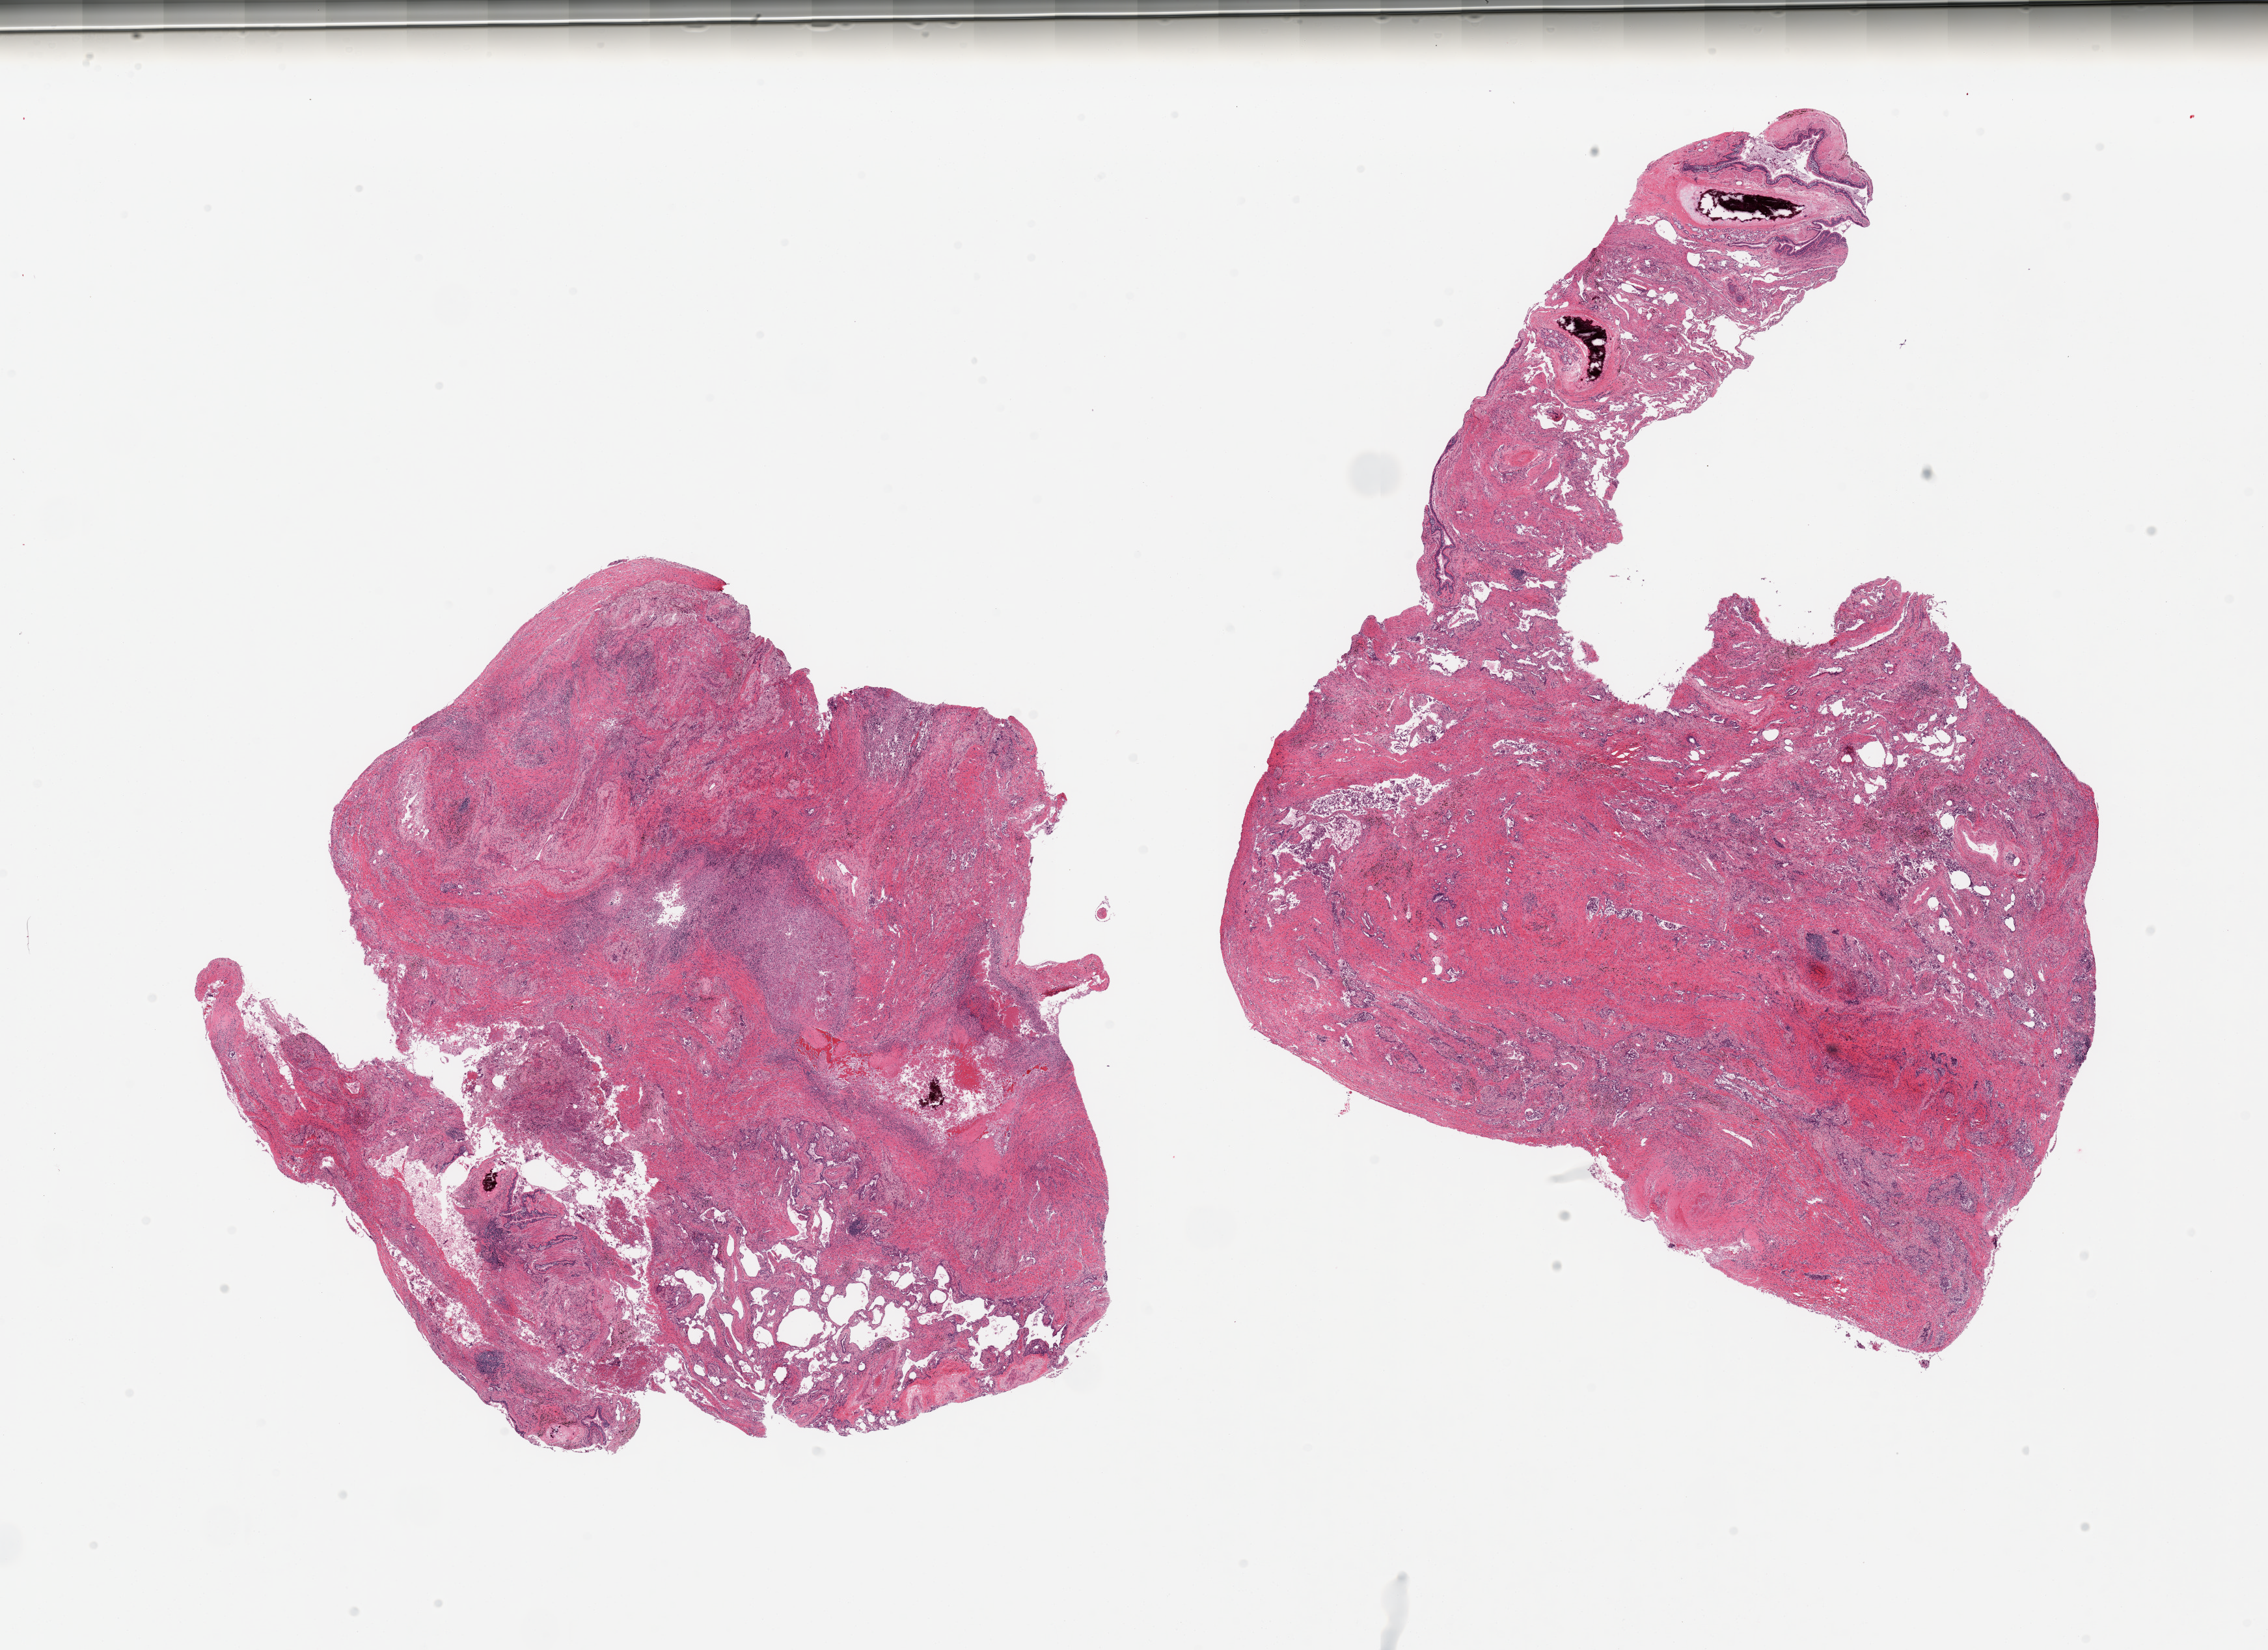
Whole-slide image, H&E stain, brightfield, low-resolution overview of the scanned area, about 27.6 x 20.1 mm (acquisition: 20x scan); PAXgene-fixed paraffin-embedded (PFPE) section; sampled site (target tissue): lung; tissue donor sample.
Pathologist's review note for this sample: 2 pieces diffuse fibrosing and acute pneumonitis, severe, focally necrotizing.